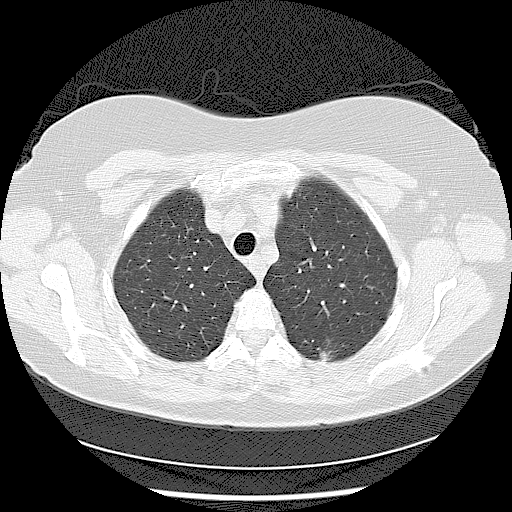
Chest CT (low-dose screening protocol), one axial image, baseline annual screen, lung window (W 1500 / L -600 HU), 2.5 mm slice thickness, lung (sharp) reconstruction kernel (LUNG), slice 22 of 116 in the series. Female participant, aged 56 years at enrolment.
Lesion marked by an expert reader, box from (x=297, y=328) to (x=348, y=373) px. The screening reader recorded 2 non-calcified nodules or masses ≥4 mm on this exam (left lower lobe, left lower lobe); which of them this box marks is not recorded. Official screen result: positive, change unspecified: nodule(s) >= 4 mm or enlarging nodule(s), mass(es), or other non-specific abnormalities suspicious for lung cancer. Lung cancer was diagnosed 638 days after this screen: adenocarcinoma, NOS, left lower lobe, moderately differentiated (G2), stage IIA (AJCC 6th edition), 15 mm at pathology.